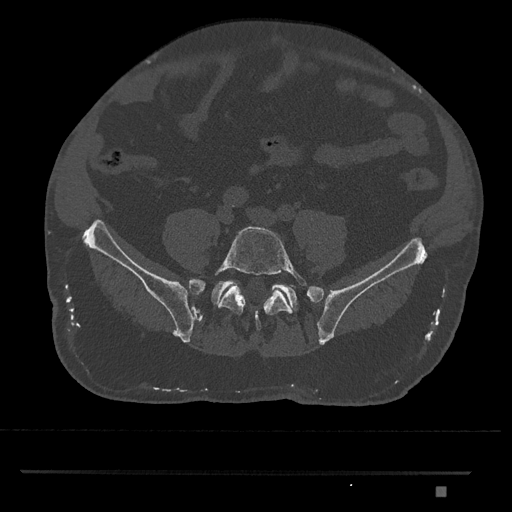
CT including the spine, one axial slice; position 545 of 1134 along the scan axis; reconstruction kernel Br40s/3; bone window (W 1800 / L 400 HU); 0.5 mm slice thickness; 512 × 512 image matrix, field of view 429 × 429 mm. Male patient, age 65 years. Case-level facts recorded for this patient, not image findings: primary cancer: prostate.
Outlined on this slice (semi-automatically segmented with operator editing):
- L5 vertebra: box from (x=213, y=226) to (x=310, y=331) px